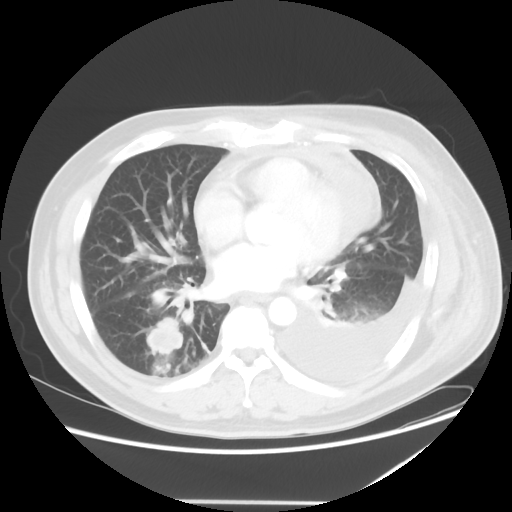
Chest CT, one axial slice; slice 22 of 52 in the series (ordered by position); reconstruction kernel STANDARD; 120 kVp; lung window (W 1500 / L -600 HU); 512 × 512 image matrix, field of view 405 × 405 mm. Patient: male, 42 years. Case-level facts recorded for this patient, not image findings: clinical TNM (as recorded): T2 N1 M1.
Annotated regions visible in this slice (rectangle marked by the reading radiologist):
- lung tumour (recorded histology: adenocarcinoma): bounding box (x1, y1, x2, y2) in pixels: (144, 317, 191, 354)